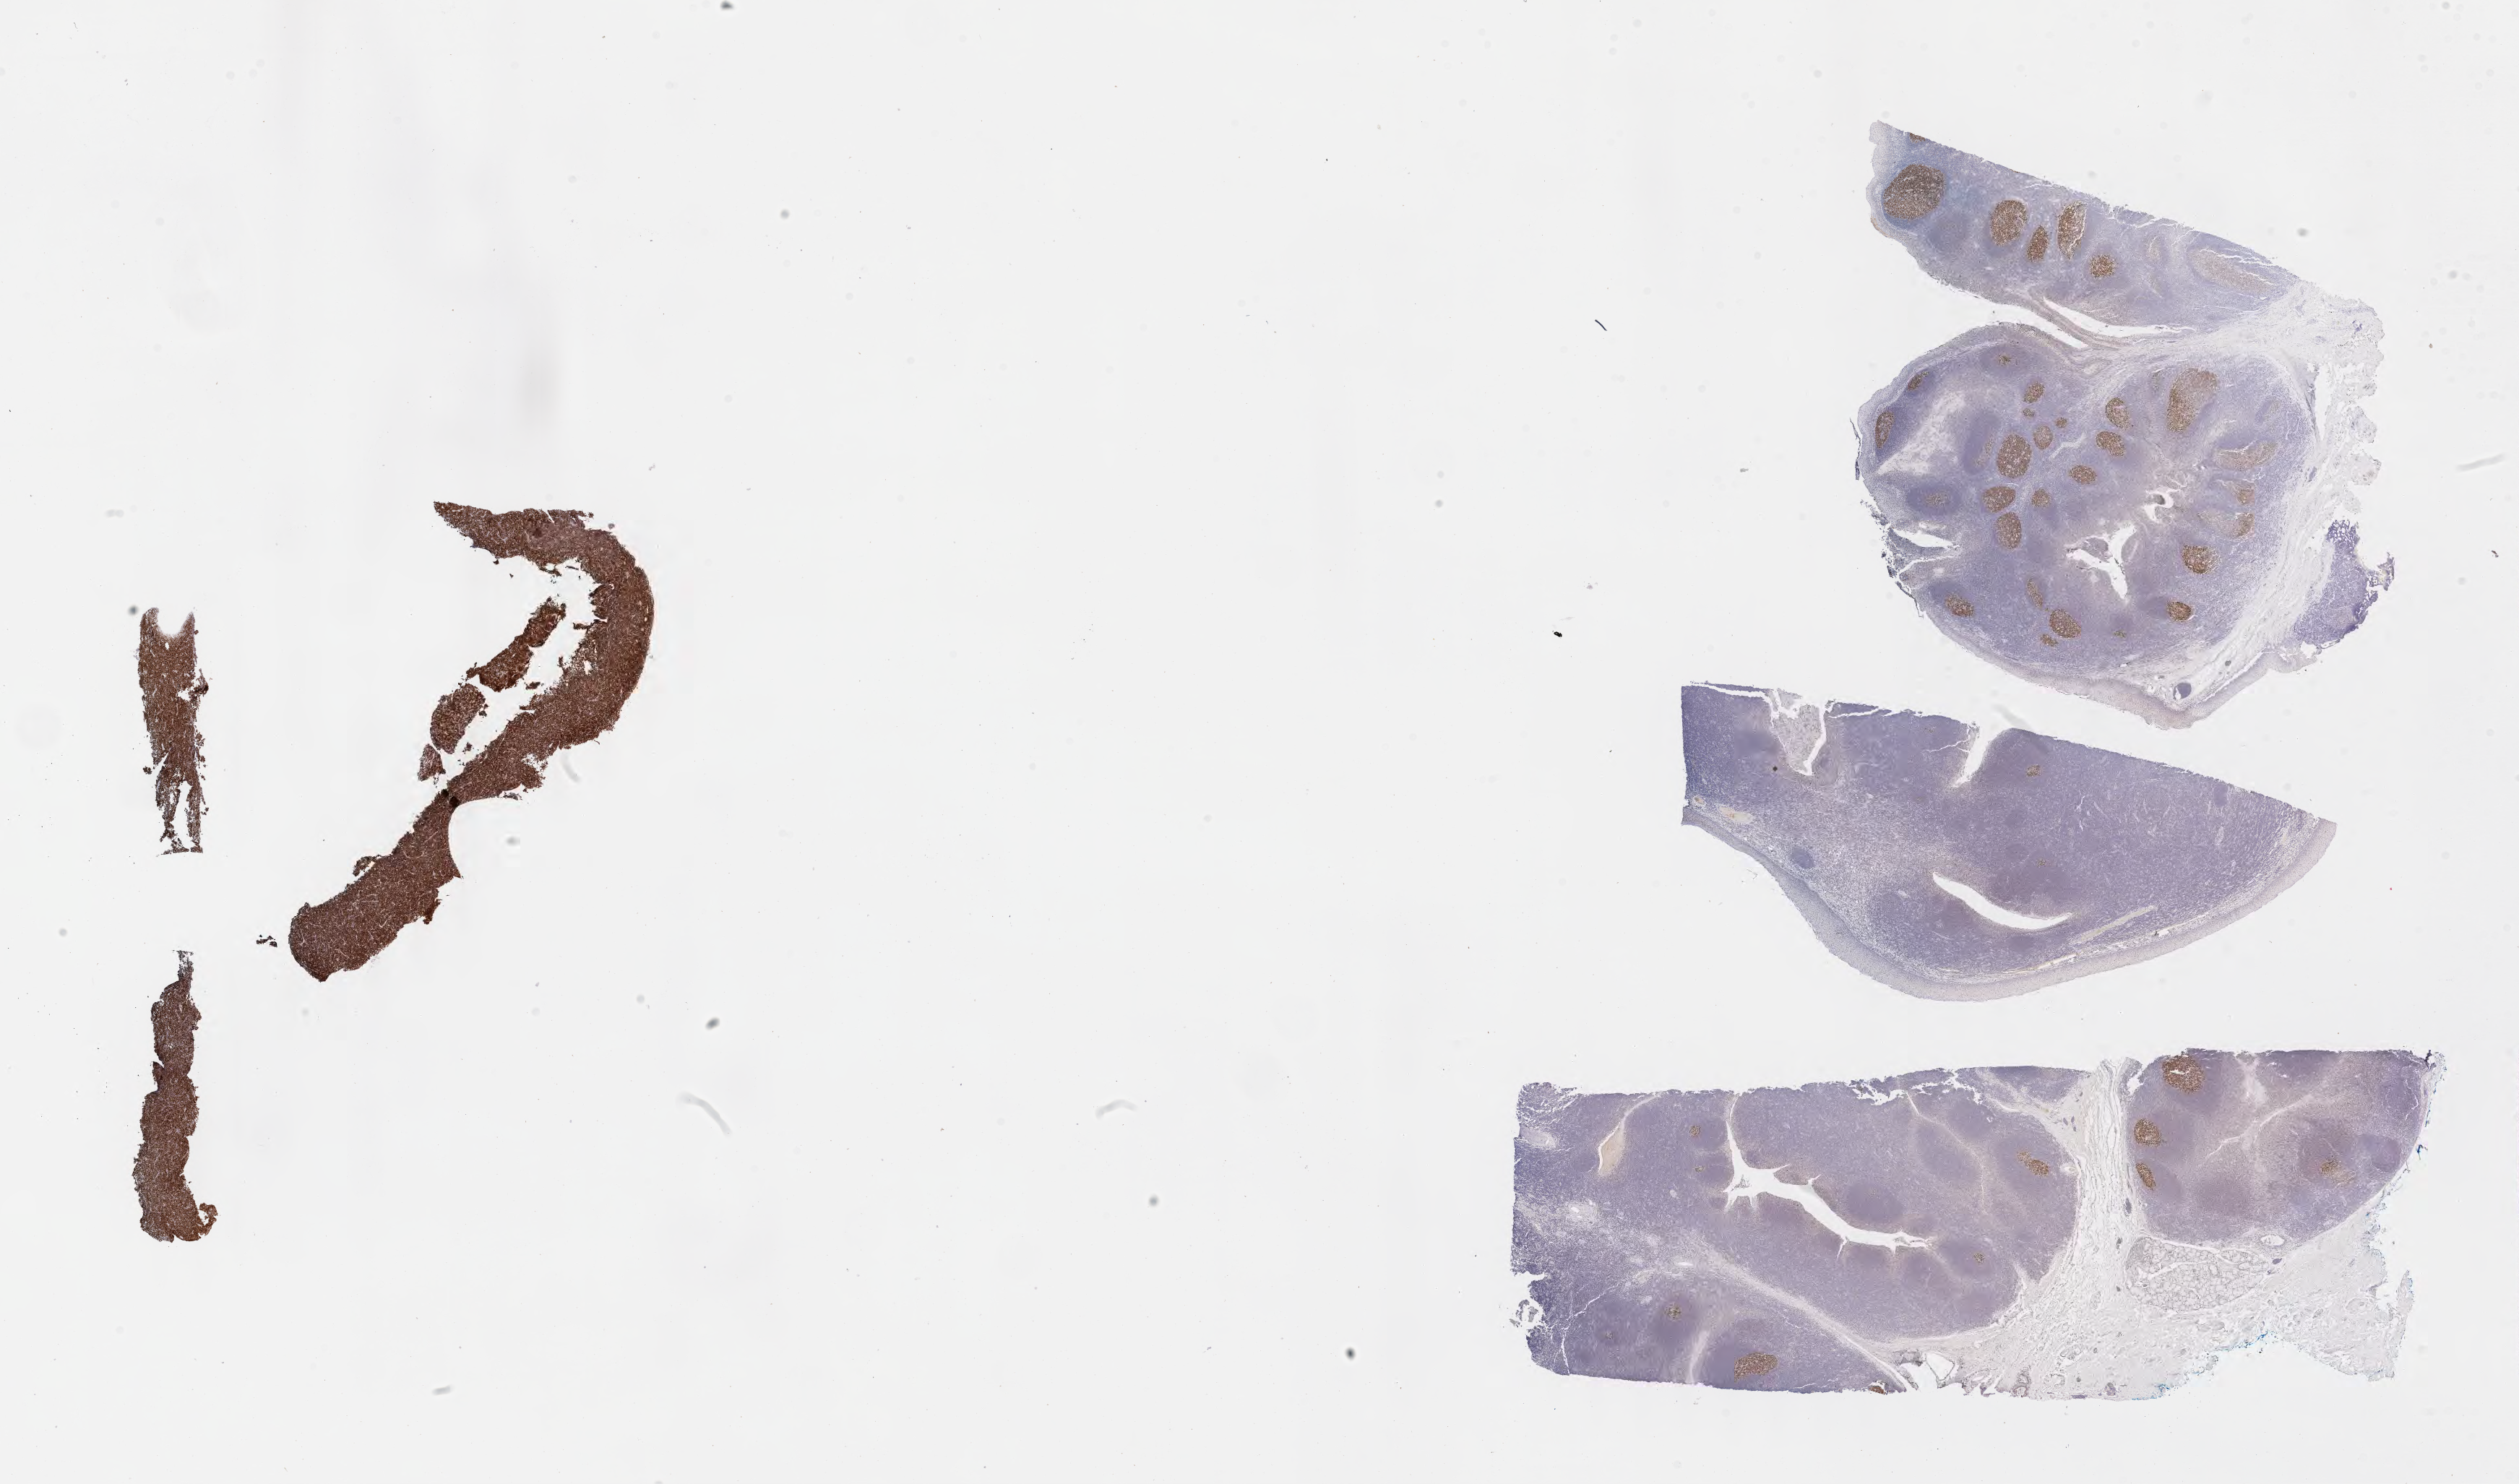
Whole-slide image, immunohistochemical stain for BCL6, low-resolution overview of the scanned area, about 28.2 x 16.6 mm, specimen: tumor tissue, site: peritoneum. Patient: female, age at initial diagnosis 7 years.
Diagnosis: Burkitt lymphoma, NOS.